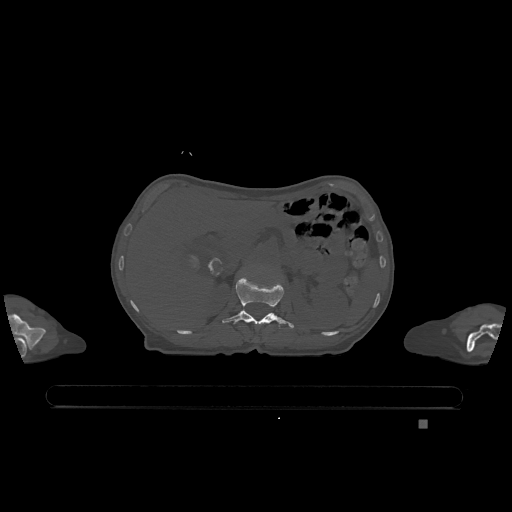
CT including the spine, one axial slice; position 471 of 1317 along the scan axis; bone window (W 1800 / L 400 HU); 0.5 mm slice thickness; 512 × 512 image matrix, field of view 500 × 500 mm. Patient: female, 74 years. From the clinical record (not read from this slice): primary cancer: lung; vertebrae with lytic lesions (as recorded): T1, T4, T5, T6, L4, L5.
Outlined on this slice (semi-automatic segmentation, software-assisted and operator-edited):
- L1 vertebra: box from (x=222, y=276) to (x=294, y=329) px